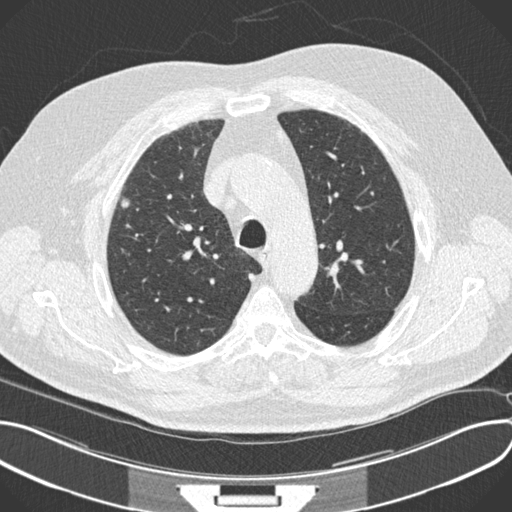
Low-dose screening chest CT, one axial slice. Position 160 of 212 along the scan axis. Reconstruction kernel B30f. 120 kVp. Lung window (W 1500 / L -600 HU). 2 mm slice thickness. 512 × 512 image matrix, field of view 380 × 380 mm.
Annotated regions visible in this slice (manually delineated by an expert):
- lesion 1 (tumor, upper lobe of right lung): box from (x=121, y=199) to (x=129, y=208) px